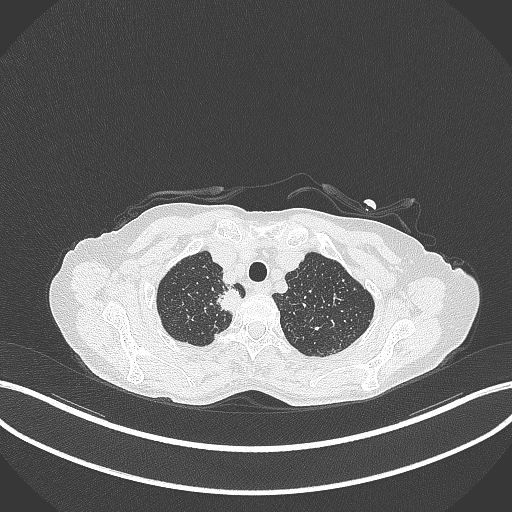
Chest CT, one axial slice; position 325 of 403 along the scan axis; reconstruction kernel B70f; 120 kVp; lung window (W 1500 / L -600 HU); 1 mm slice thickness; 512 × 512 image matrix. Patient: female, 75 years. Case-level facts recorded for this patient, not image findings: clinical TNM (as recorded): T1c N1 M1.
Outlined on this slice (bounding box drawn by a radiologist):
- lung tumour (recorded histology: adenocarcinoma): bounding box (x1, y1, x2, y2) in pixels: (218, 285, 246, 318)